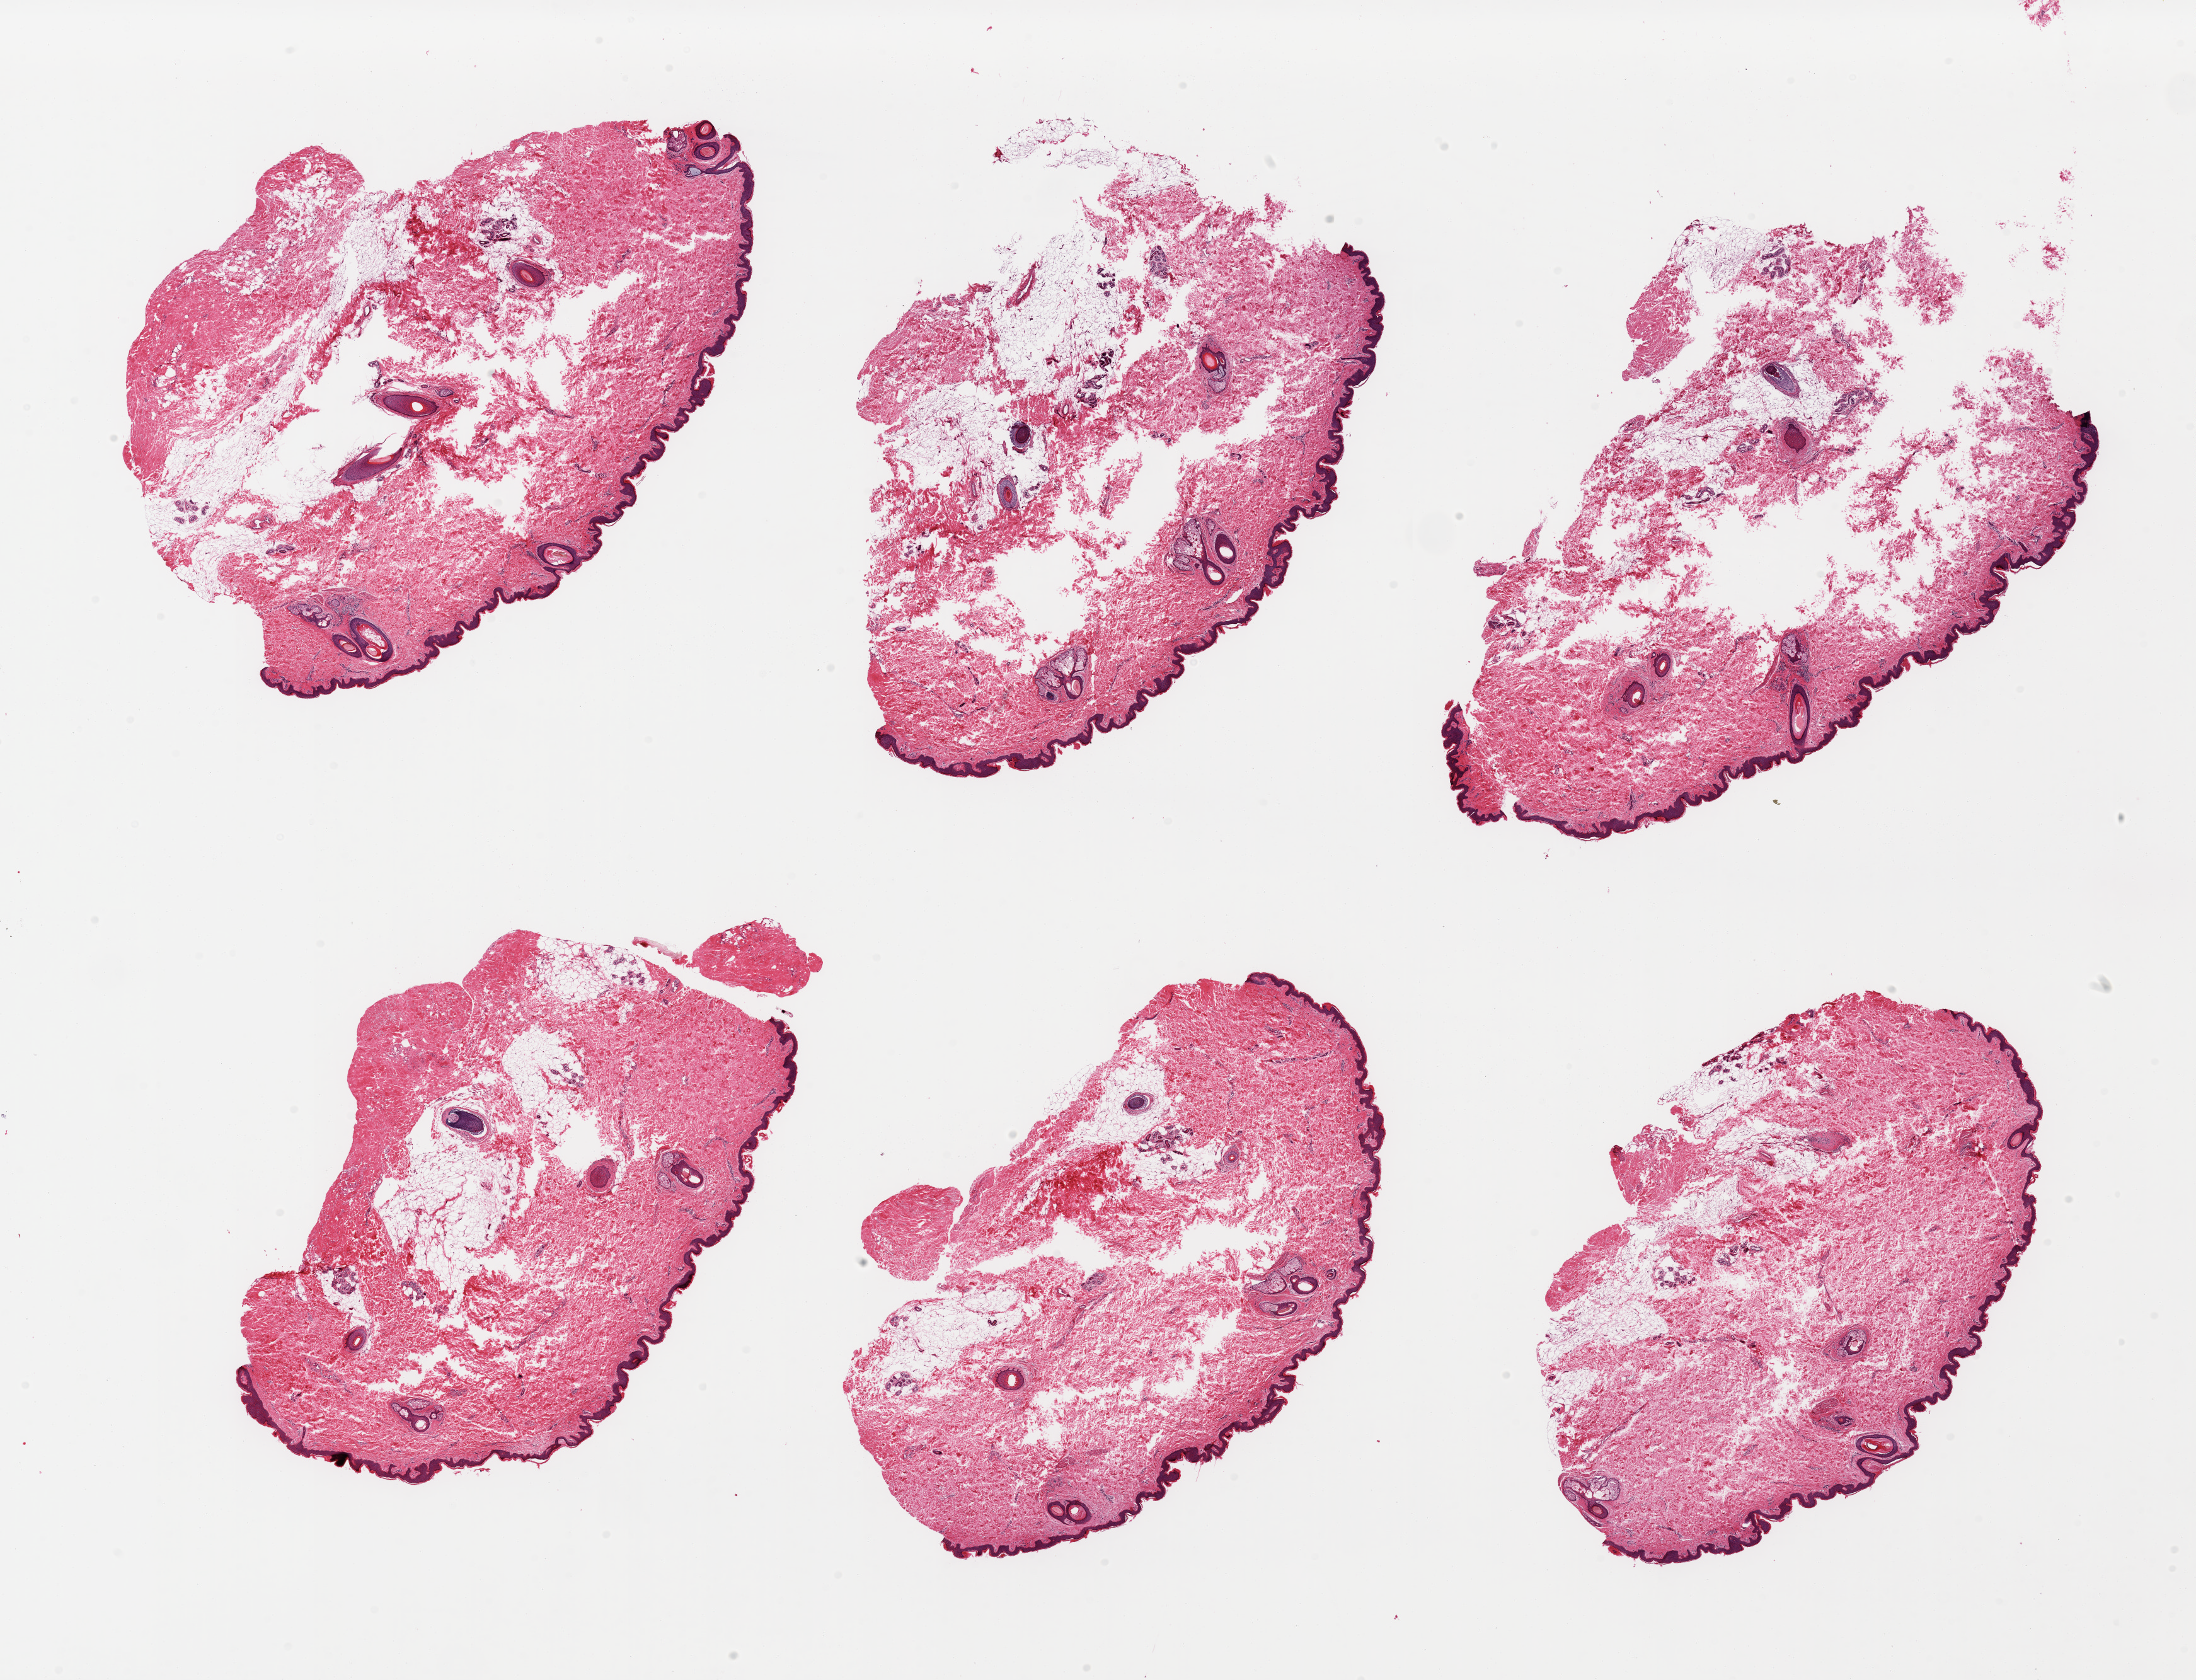
Hematoxylin and eosin (H&E) whole-slide image, brightfield — a low-resolution overview of the entire scanned area, about 27.6 x 21.1 mm, PAXgene-fixed paraffin-embedded (PFPE) section, section of skin of suprapubic region (target tissue), donor tissue sample.
Reviewer comment on this tissue sample: 6 pieces, moderate dermal fat; squamous epithelium is ~40-50 microns.